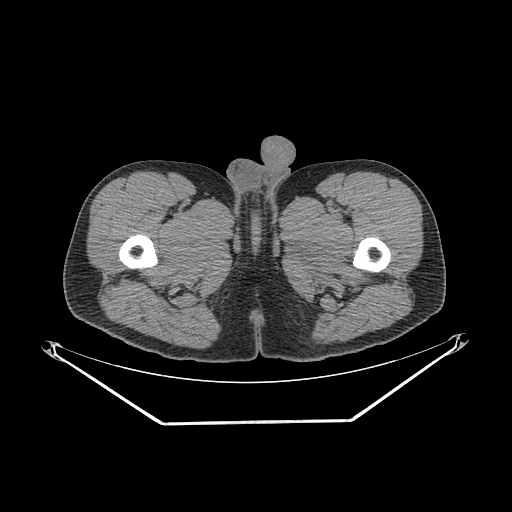
CT of an extremity soft-tissue mass (from a PET/CT study), one axial slice; position 265 of 267 along the scan axis; 140 kVp; soft-tissue window (W 400 / L 40 HU); 512 × 512 image matrix, field of view 500 × 500 mm. Male patient. From the clinical record (not read from this slice): histological type: extraskeletal osteosarcoma; grade: high; site of the primary tumour: left adductur.
Outlined on this slice (expert contour drawn on MRI and transferred to this co-registered scan by the dataset authors):
- gross tumour volume (mass): bounding box <283,198,385,296> (left, top, right, bottom; pixels)